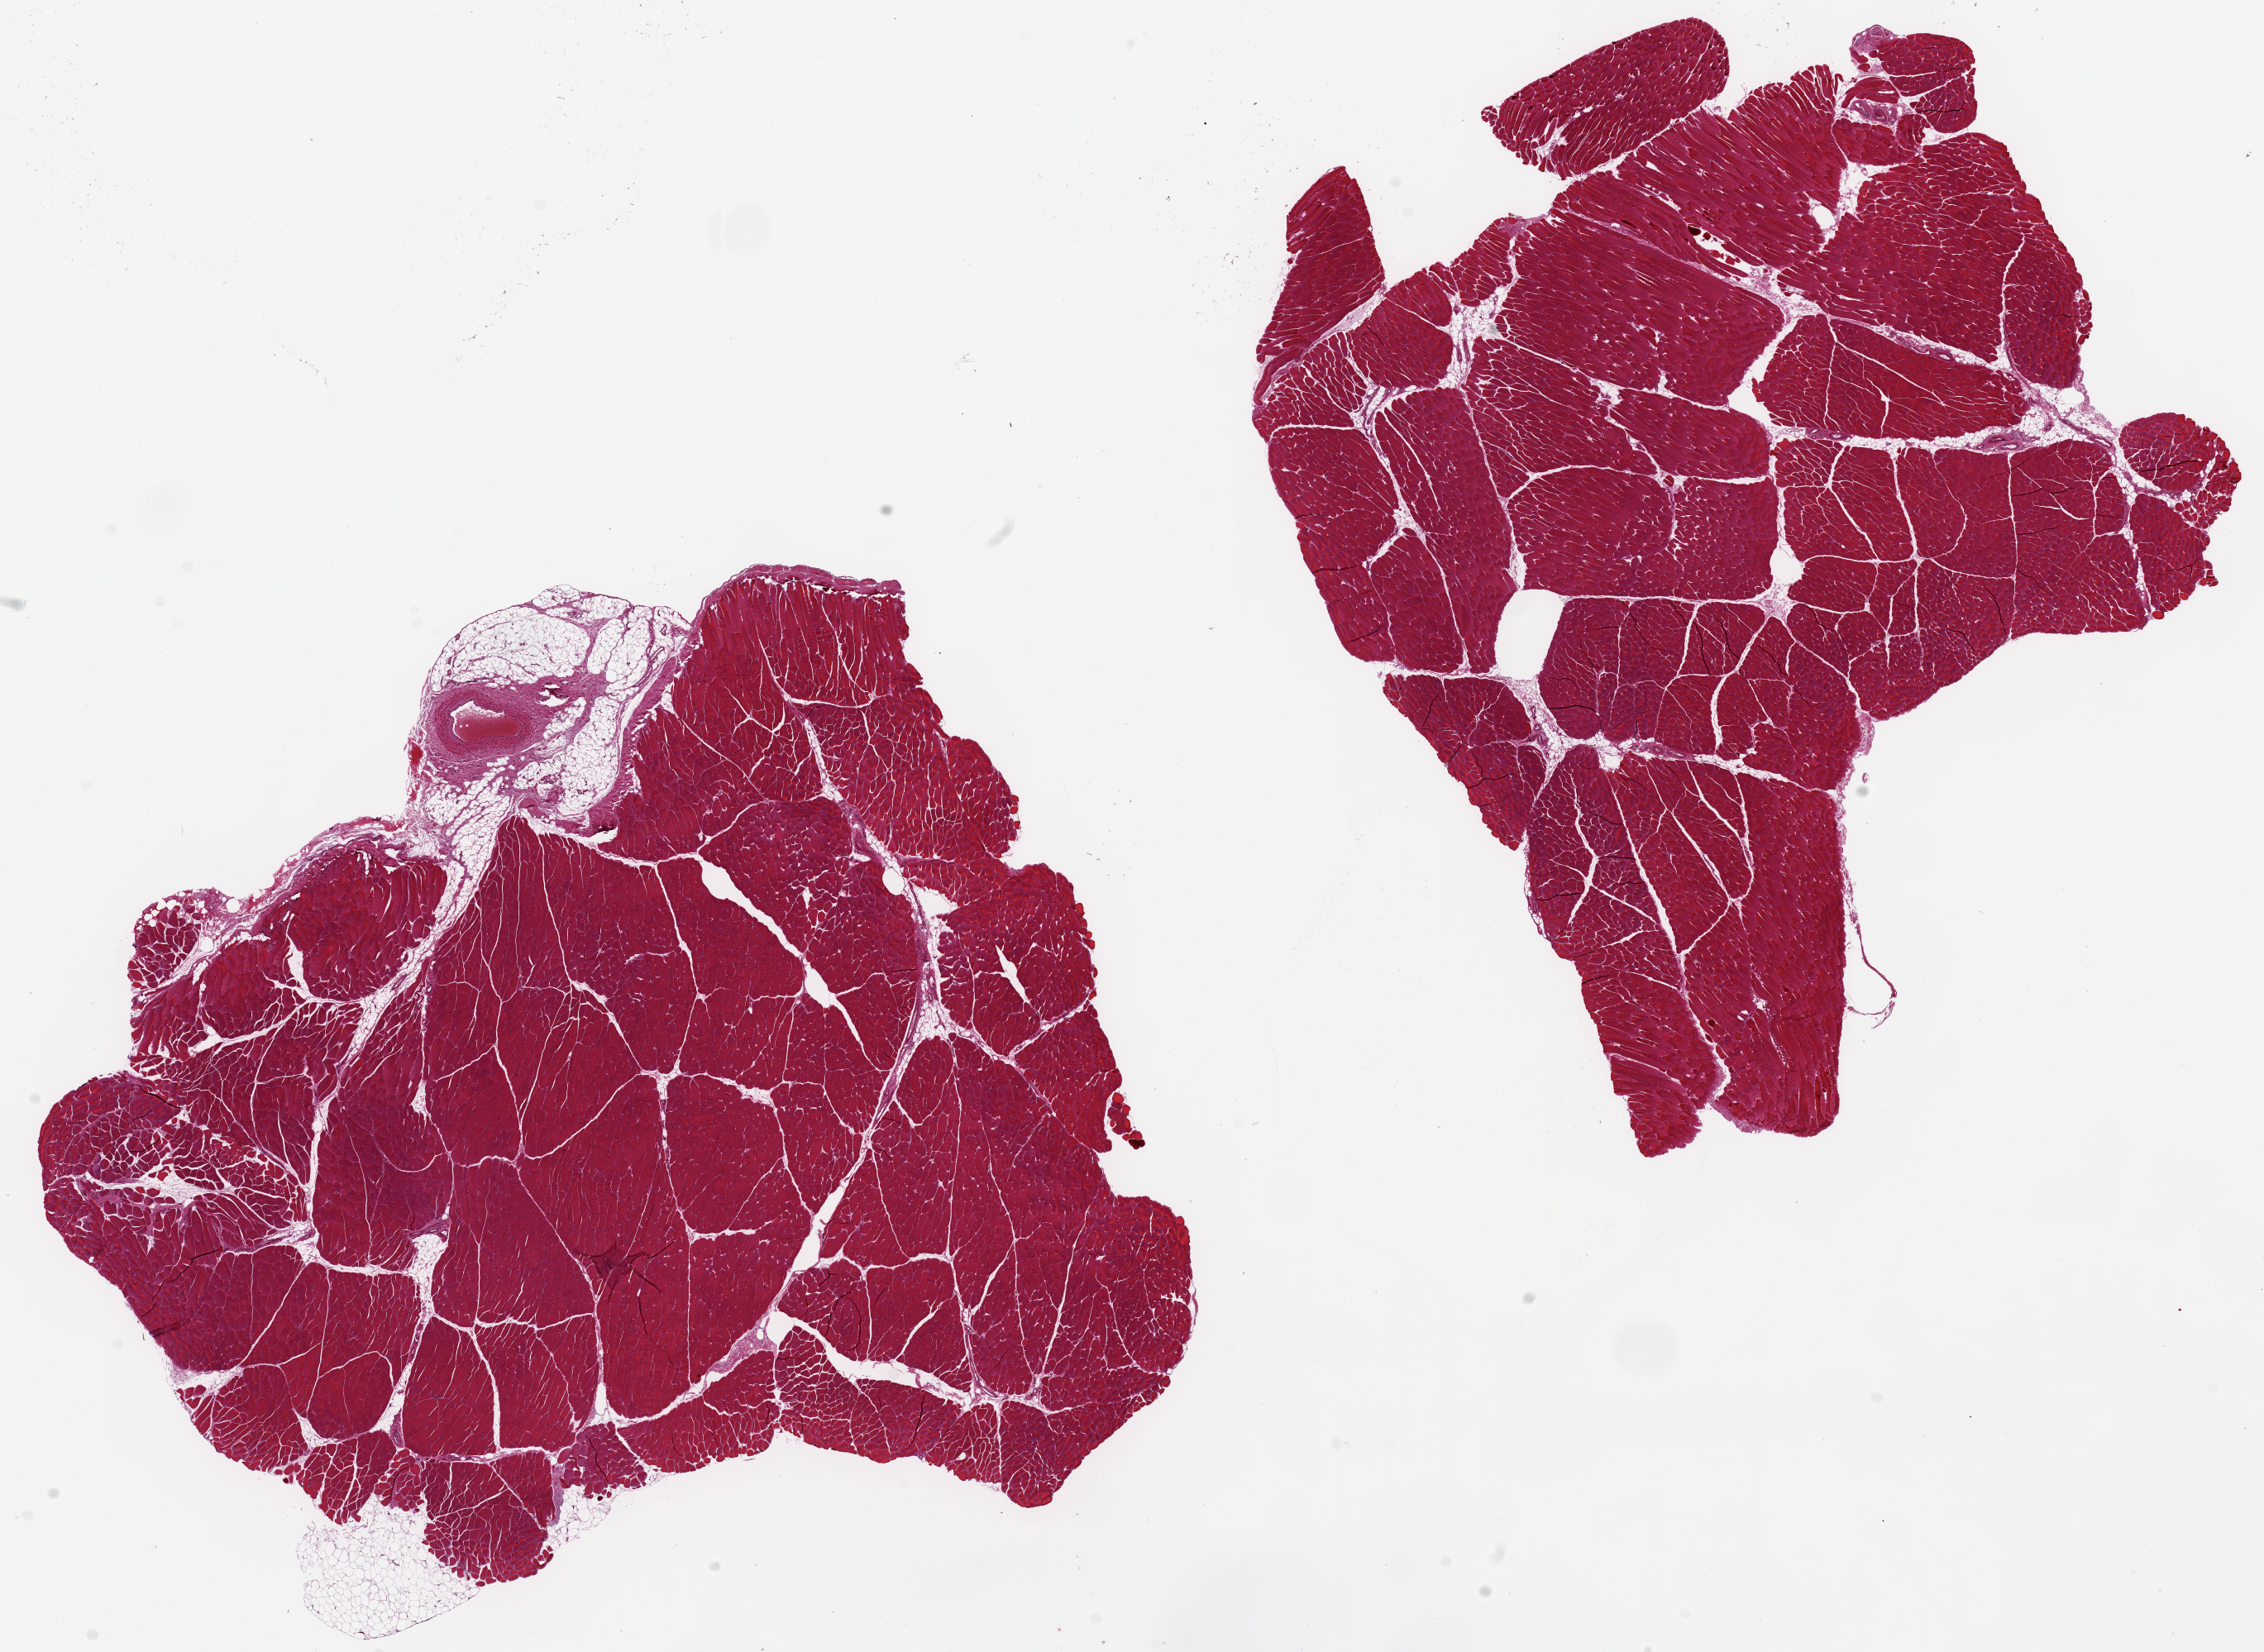
H&E whole-slide image, whole scanned area (about 21.7 x 15.8 mm, from a 20x scan) shown as a low-resolution overview, PAXgene-fixed paraffin-embedded (PFPE) section, section of skeletal muscle (target tissue), tissue donor sample. Donor: female.
Pathologist's review note for this sample: 2 pieces, 10x10 & 10x8mm; 1 piece has 10% adipose on edge.